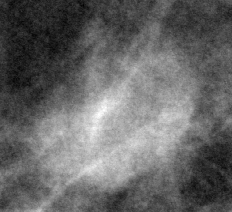
Region of interest cut from a scanned film mammogram (one marked finding), right breast, MLO view, BI-RADS breast density category 1 (scale 1–4).
Finding: mass, shape lobulated, margins circumscribed / ill defined; BI-RADS assessment category 4; subtlety rating 3 on a 1 (subtle) to 5 (obvious) scale; pathology (as recorded): benign.